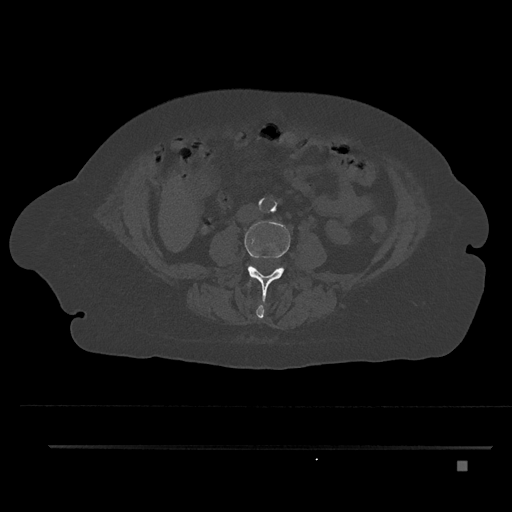
CT including the spine, one axial slice. Slice 124 of 797 in the series (ordered by position). Reconstruction kernel Br40s/3. Bone window (W 1800 / L 400 HU). 512 × 512 image matrix, field of view 437 × 437 mm. Patient: female, 76 years. From the clinical record (not read from this slice): primary cancer: lung.
Structures marked on this image (semi-automatic segmentation, software-assisted and operator-edited):
- L2 vertebra: bounding box (x1, y1, x2, y2) in pixels: (247, 279, 264, 320)
- L3 vertebra: (245, 221, 290, 305)